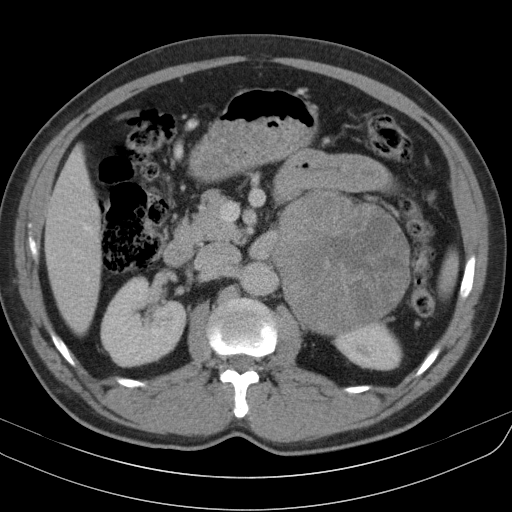
Contrast-enhanced abdominal CT, one axial slice; position 62 of 91 along the scan axis; reconstruction kernel B31s; intravenous contrast given; soft-tissue window (W 400 / L 40 HU); 5 mm slice thickness; 512 × 512 image matrix, field of view 370 × 370 mm. Male patient, age 51 years. From the clinical record (not read from this slice): diagnosis: adrenocortical carcinoma; tumour side: left adrenal; tumour size at pathology: 18 cm; Ki-67 index: 40 %; stage (as recorded): 3.
Structures marked on this image (semi-automatic segmentation, software-assisted and operator-edited):
- mass: box from (x=278, y=193) to (x=407, y=331) px